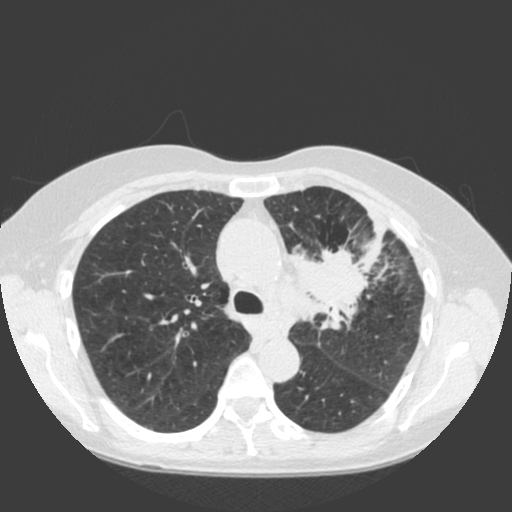
Low-dose screening chest CT, one axial slice; position 131 of 184 along the scan axis; lung window (W 1500 / L -600 HU); 512 × 512 image matrix, field of view 350 × 350 mm.
Structures marked on this image (expert manual segmentation):
- lesion 1 (tumor, hilum of left lung): bounding box [x1, y1, x2, y2] px = [287, 214, 386, 331]